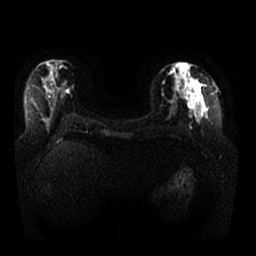
Breast MRI, one axial slice. Slice 11 of 25 in the series (ordered by position). Diffusion-weighted series; image 2 of 4 stored at this slice position (different b-values; order by instance number). 1.5 T. 4 mm slice thickness. 256 × 256 image matrix, field of view 350 × 350 mm. Female patient.
Structures marked on this image (expert manual segmentation):
- tumour on diffusion-weighted imaging: bounding box <182,88,194,105> (left, top, right, bottom; pixels)